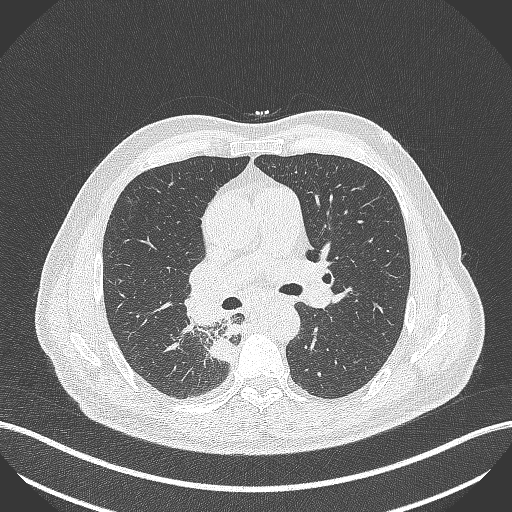
Chest CT, one axial slice. Slice 273 of 451 in the series (ordered by position). Lung window (W 1500 / L -600 HU). 512 × 512 image matrix, field of view 400 × 400 mm. Patient: male, 61 years. Case-level facts recorded for this patient, not image findings: clinical TNM (as recorded): T1 N0 M0.
Outlined on this slice (bounding box drawn by a radiologist):
- lung tumour (recorded histology: small cell carcinoma): bounding box (x1, y1, x2, y2) in pixels: (207, 333, 240, 367)